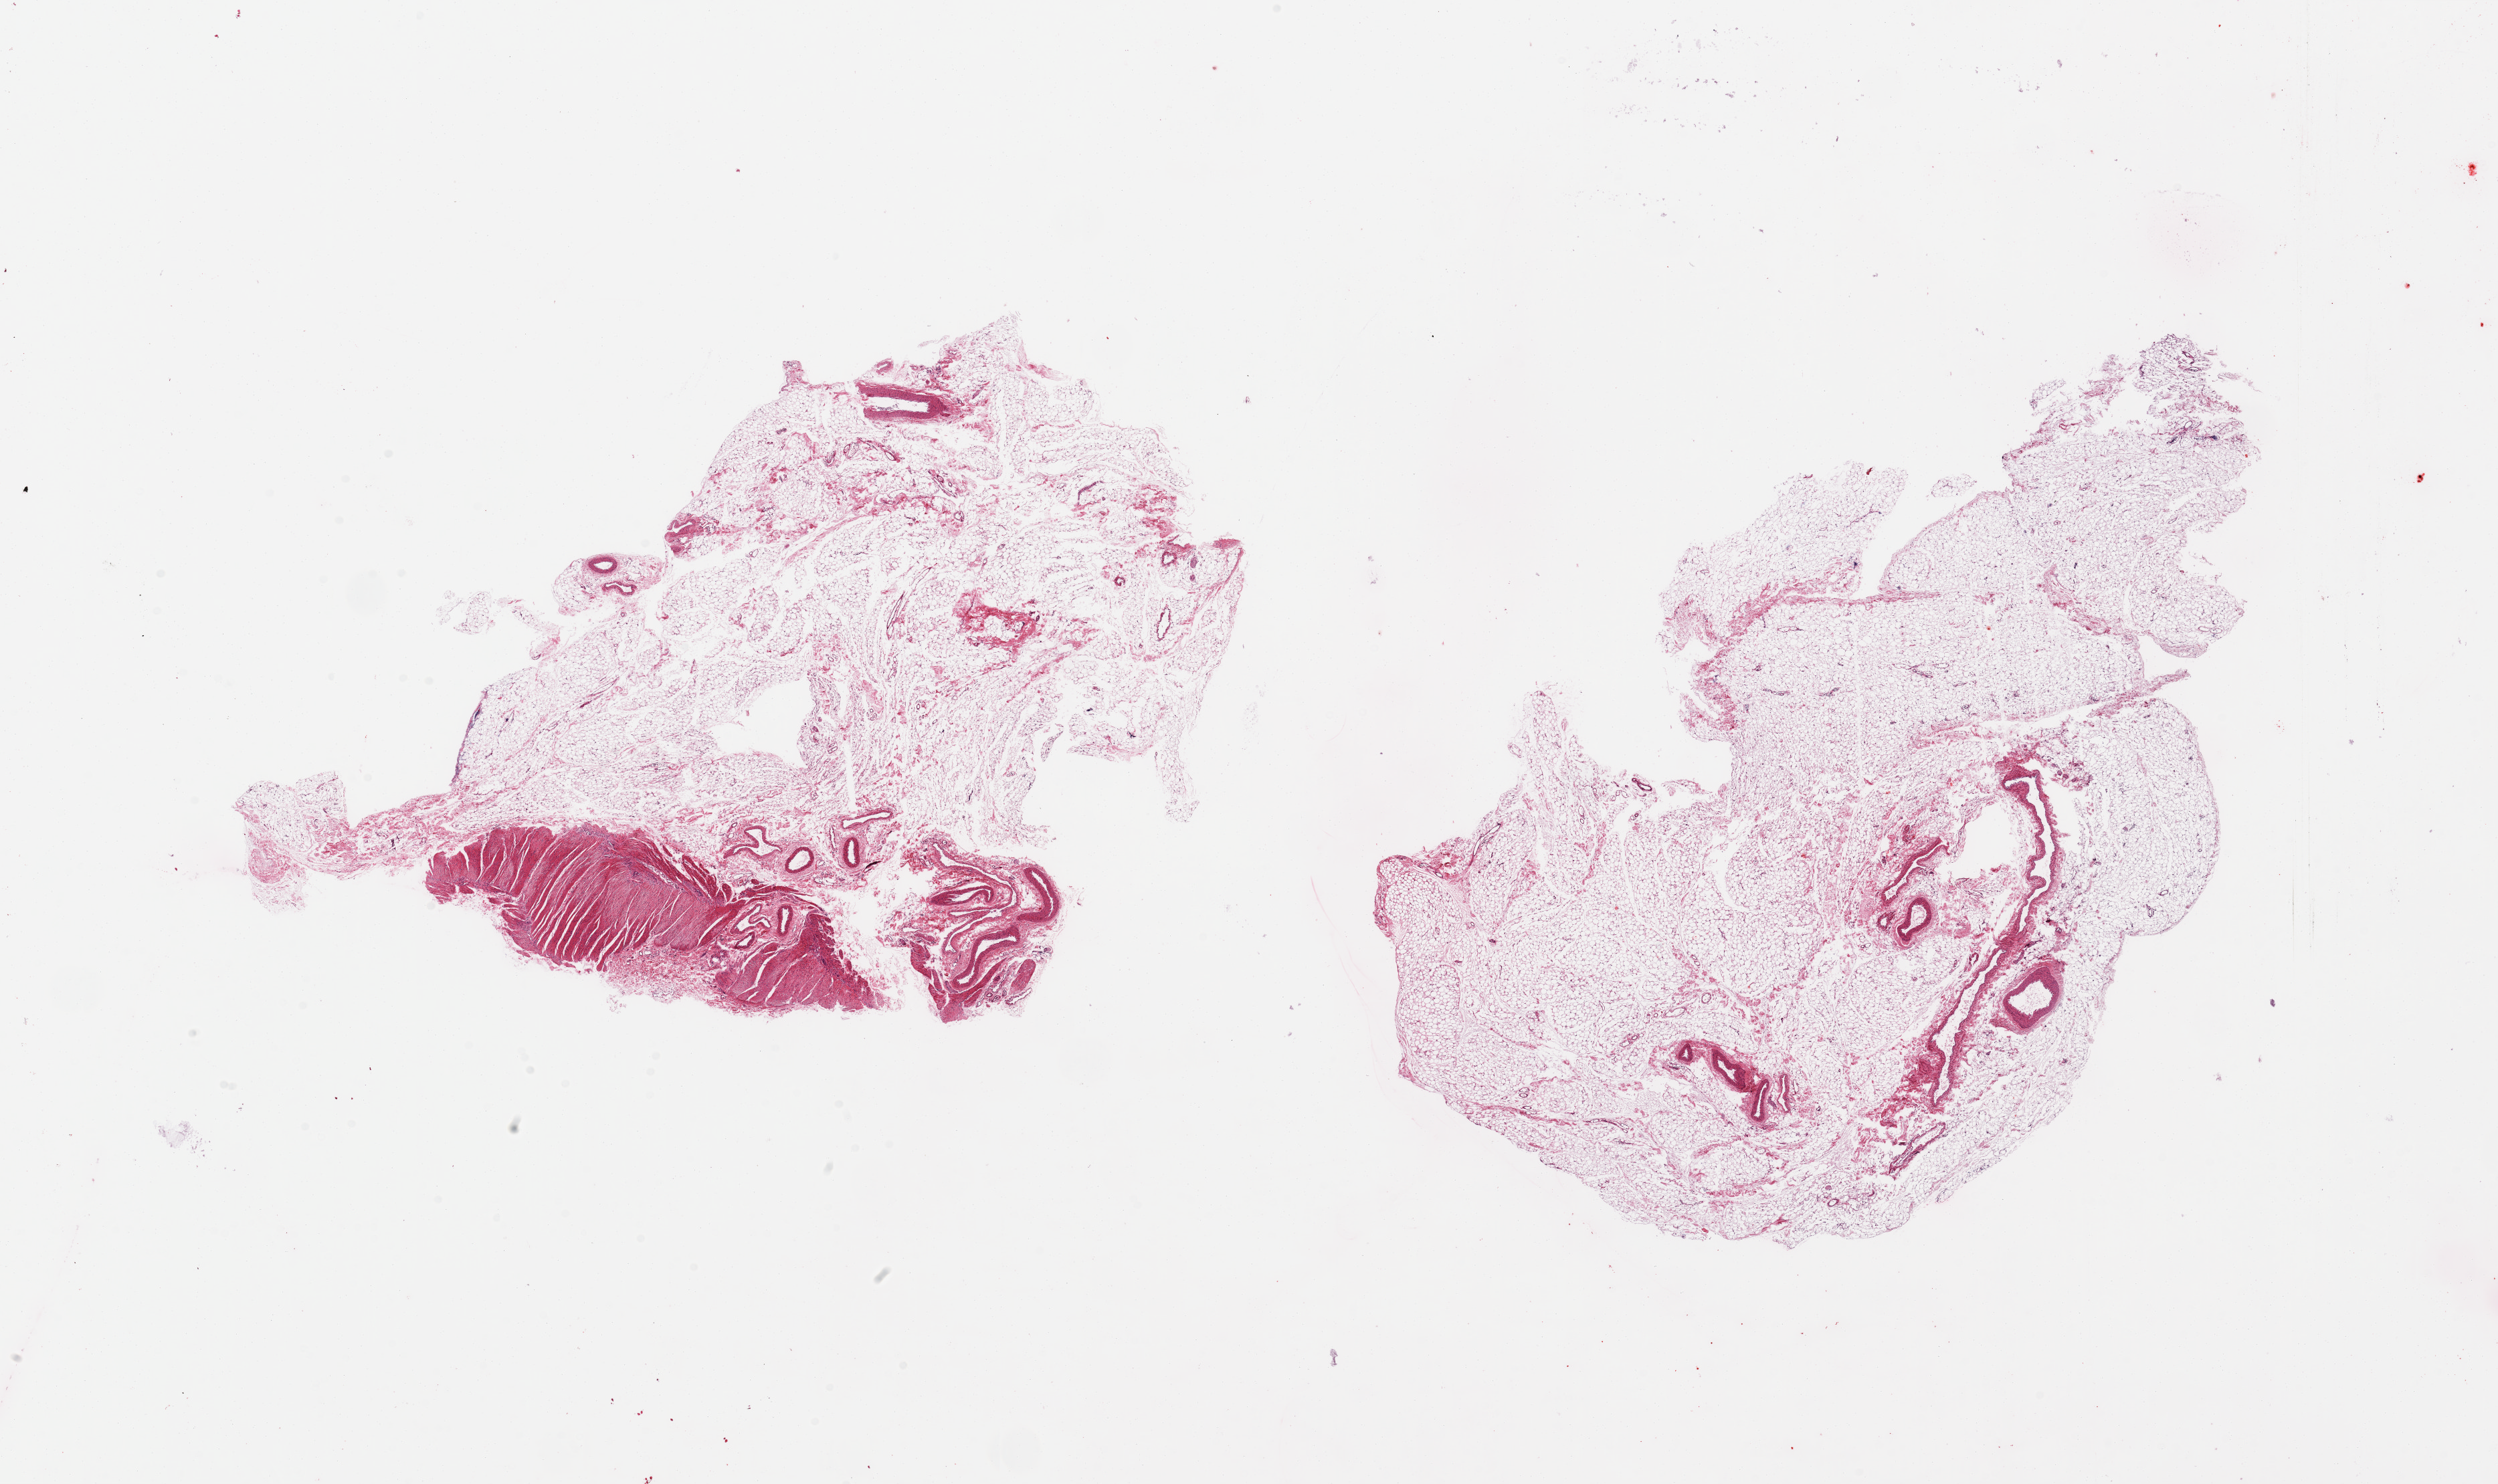
Digitized hematoxylin and eosin (H&E)-stained section — shown as a low-resolution overview of the whole scanned area (about 29.5 x 17.6 mm), PAXgene-fixed paraffin-embedded (PFPE) section, target tissue: omentum, tissue donor sample. Donor: male.
Pathologist's review note for this sample: 2 pieces; predominantly fat, but with several larger vessels and portion of muscularis.